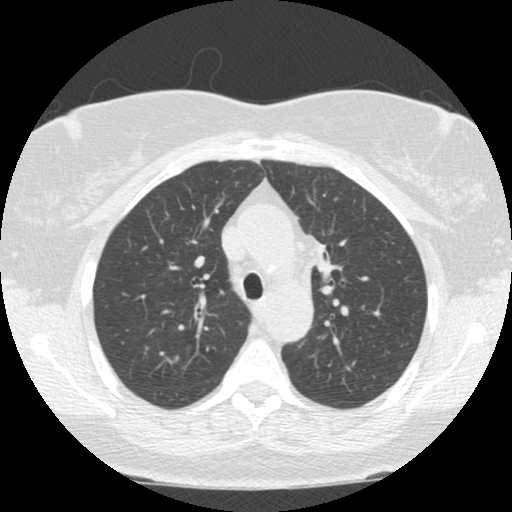
Low-dose screening chest CT, axial slice. Second annual screen. Lung window (W 1500 / L -600 HU). 2.5 mm slice thickness. Slice 41 of 120 in the series. Female, age 66 years at enrolment.
Expert reader's lesion annotation, bounding box <293,233,343,289> (left, top, right, bottom; pixels). The exam's reader record, not a measurement of the box and not confirmed to be the same lesion: non-calcified nodule or mass ≥4 mm, left upper lobe, 12 × 9 mm, smooth margins, soft tissue attenuation, pre-existing on the prior screen: no. Participant outcome: lung cancer diagnosed 196 days after this screen — small cell carcinoma, NOS, left upper lobe, stage IIIA (AJCC 6th edition), 50 mm at pathology.